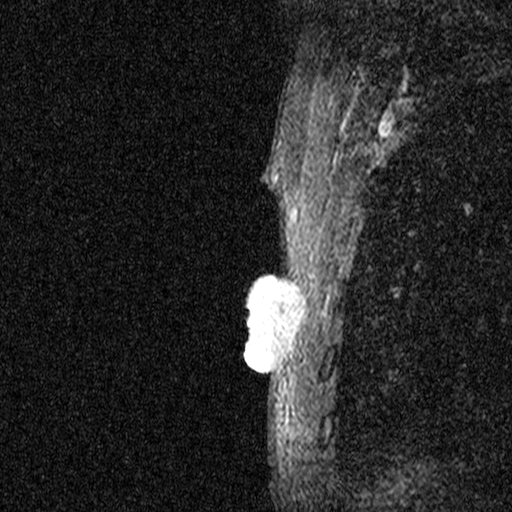
Breast MRI (dynamic contrast-enhanced), one sagittal slice. Slice 40 of 44 in the series (ordered by position). Dynamic contrast-enhanced study with each time point stored as its own series, time point 2 of 3 at this slice position (early post-contrast, ordered by acquisition time). 1.5 T. TE 4.5 ms, TR 11 ms. 2.05 mm slice thickness. 512 × 512 image matrix. Patient: female, 44 years. Case-level facts recorded for this patient, not image findings: setting: breast cancer imaged before/during neoadjuvant chemotherapy; receptor status: HR-positive, HER2-negative.
Structures marked on this image (semi-automatically segmented with operator editing):
- analysis volume of interest (the breast-tissue region the enhancement analysis was run in; not a lesion): box from (x=204, y=254) to (x=317, y=401) px
- tumour enhancement mask (voxels above the 90 % enhancement threshold inside the analysis volume of interest): (x=245, y=259)–(x=294, y=396)